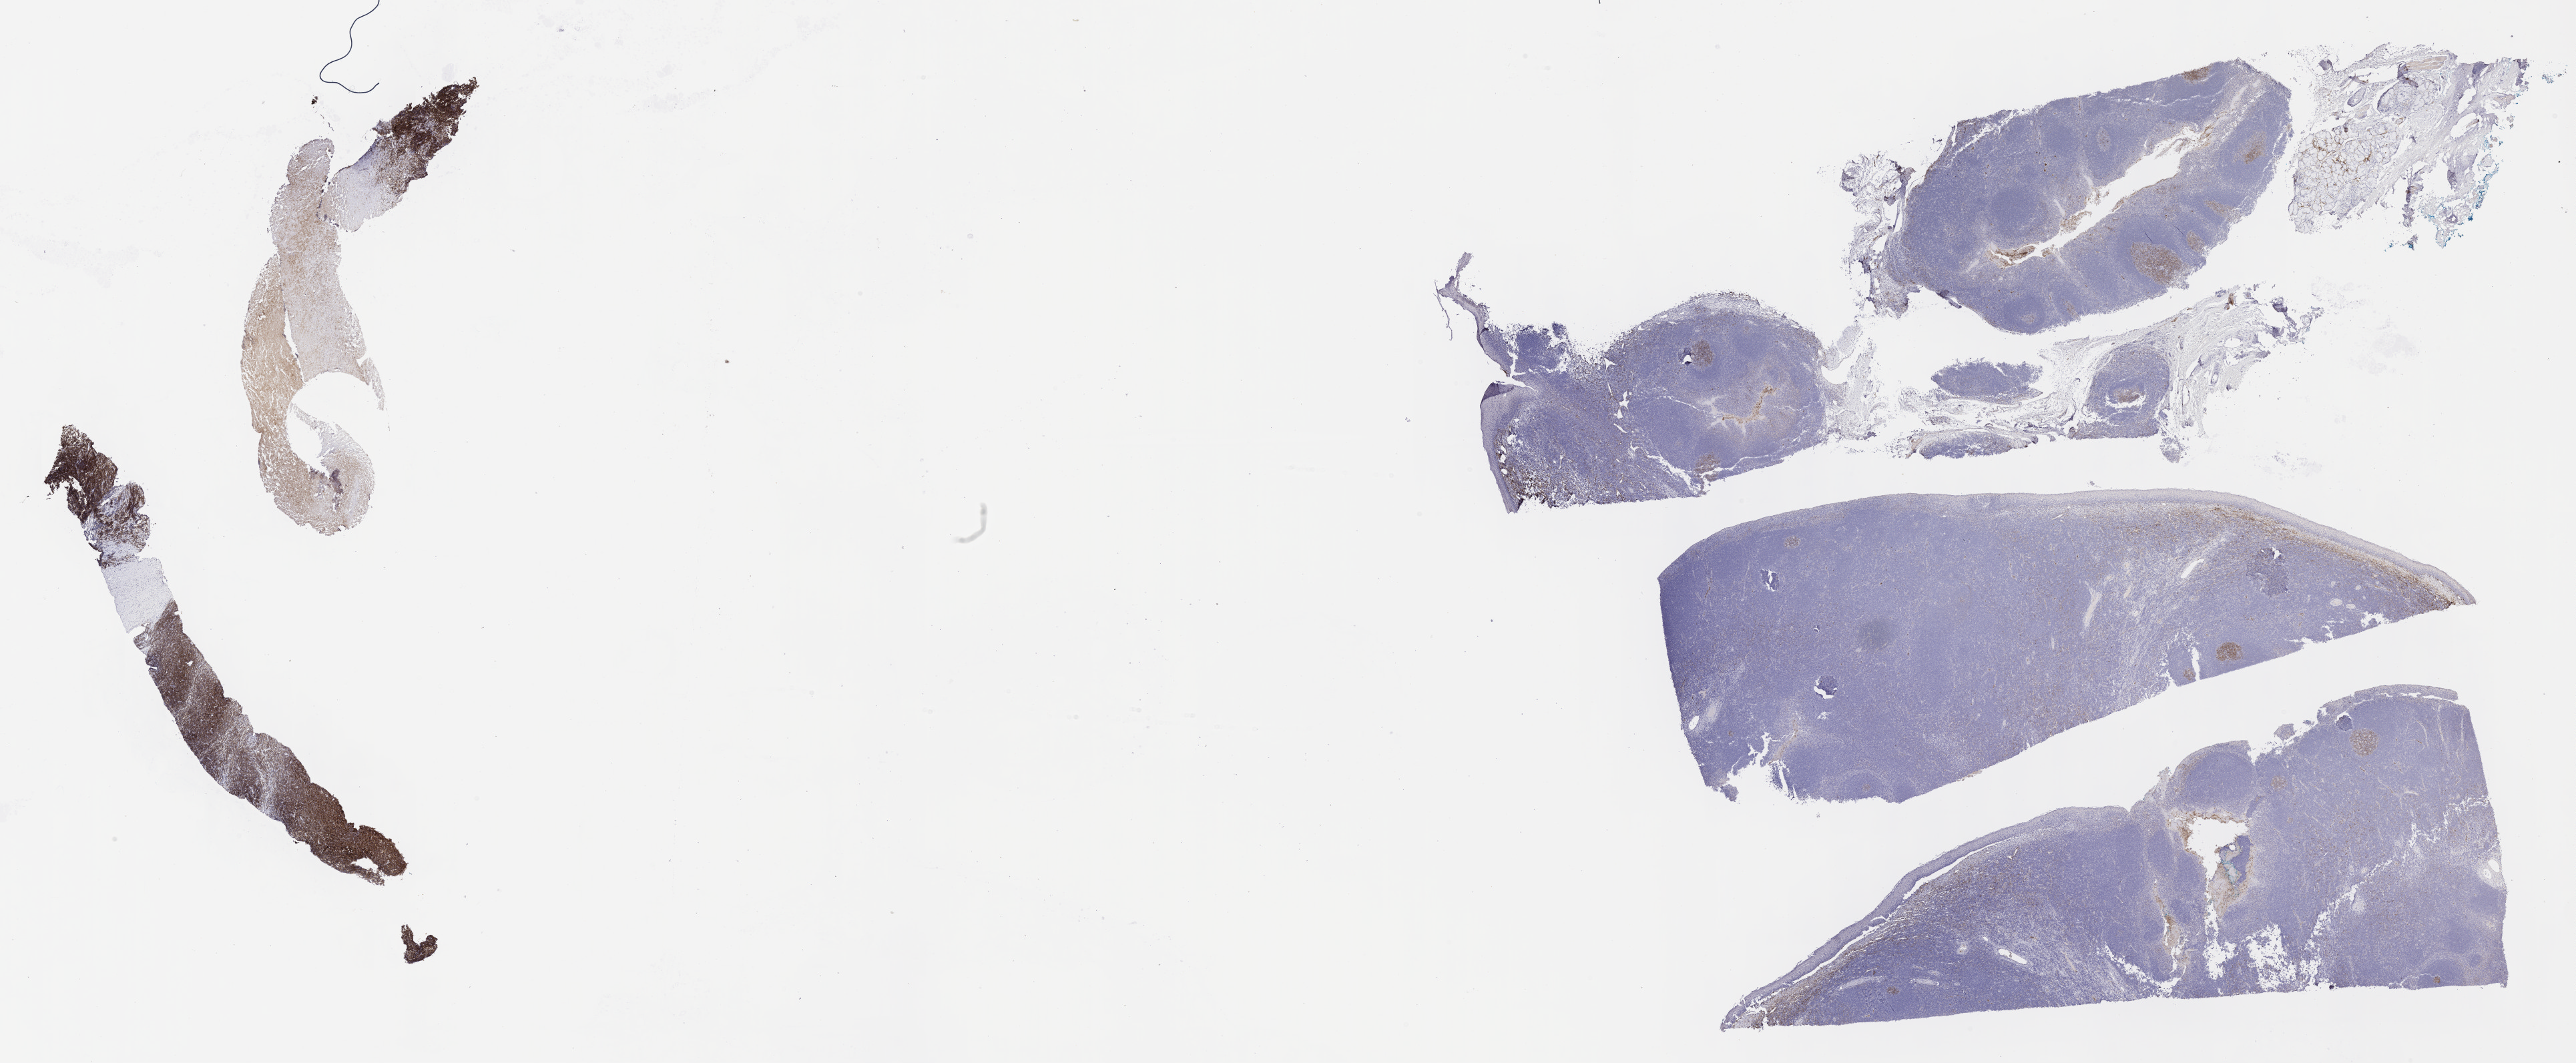
Whole-slide image, immunohistochemical stain for CD10, whole scanned area (about 31.2 x 12.9 mm) shown as a low-resolution overview, tumor tissue. Patient: male, age 10 years.
Diagnosis: Burkitt lymphoma, NOS.